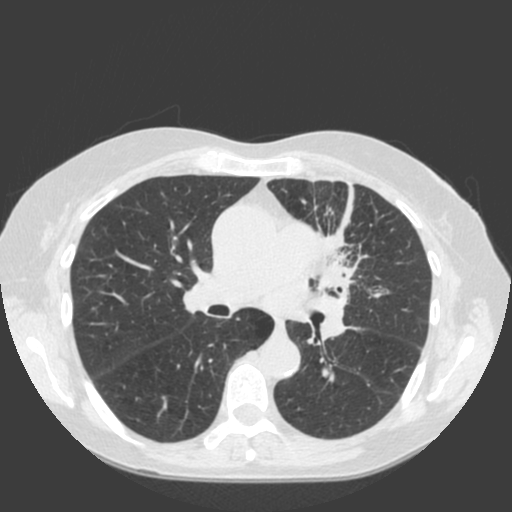
Low-dose screening chest CT, one axial slice. Slice 111 of 184 in the series (ordered by position). Lung window (W 1500 / L -600 HU). 2 mm slice thickness. 512 × 512 image matrix, field of view 350 × 350 mm.
Outlined on this slice (manually delineated by an expert):
- lesion 1 (tumor, hilum of left lung): box from (x=306, y=231) to (x=352, y=343) px